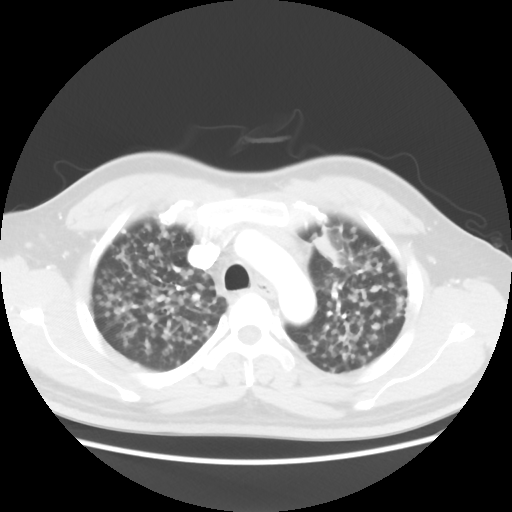
Chest CT, one axial slice; slice 30 of 40 in the series (ordered by position); reconstruction kernel STANDARD; lung window (W 1500 / L -600 HU); 5 mm slice thickness; 512 × 512 image matrix, field of view 366 × 366 mm. Male patient, age 41 years. From the clinical record (not read from this slice): clinical TNM (as recorded): T1c N3 M1b.
Annotated regions visible in this slice (bounding box drawn by a radiologist):
- lung tumour (recorded histology: adenocarcinoma): bounding box [x1, y1, x2, y2] px = [311, 227, 340, 270]